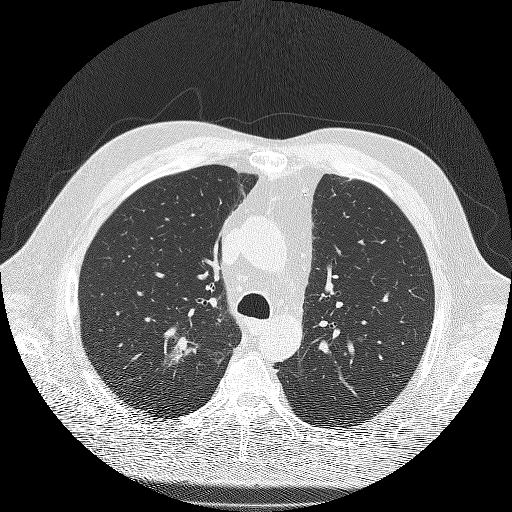
Chest CT (low-dose screening protocol), one axial image, second annual screen, lung window (W 1500 / L -600 HU), 2 mm slice thickness, slice 42 of 180 in the series. Male participant, aged 71 years at enrolment. Former smoker at enrolment.
- Expert-annotated lung lesion, bounding box (x1, y1, x2, y2) in pixels: (134, 323, 210, 389).
- The screening reader recorded 3 non-calcified nodules or masses ≥4 mm on this exam (right upper lobe, right upper lobe, right lower lobe); which of them this box marks is not recorded.
- Official screen result: positive, other.
- Lung cancer was diagnosed 59 days after this screen: bronchiolo-alveolar adenocarcinoma, NOS, right upper lobe, moderately differentiated (G2), stage IIIA (AJCC 6th edition), 25 mm at pathology.